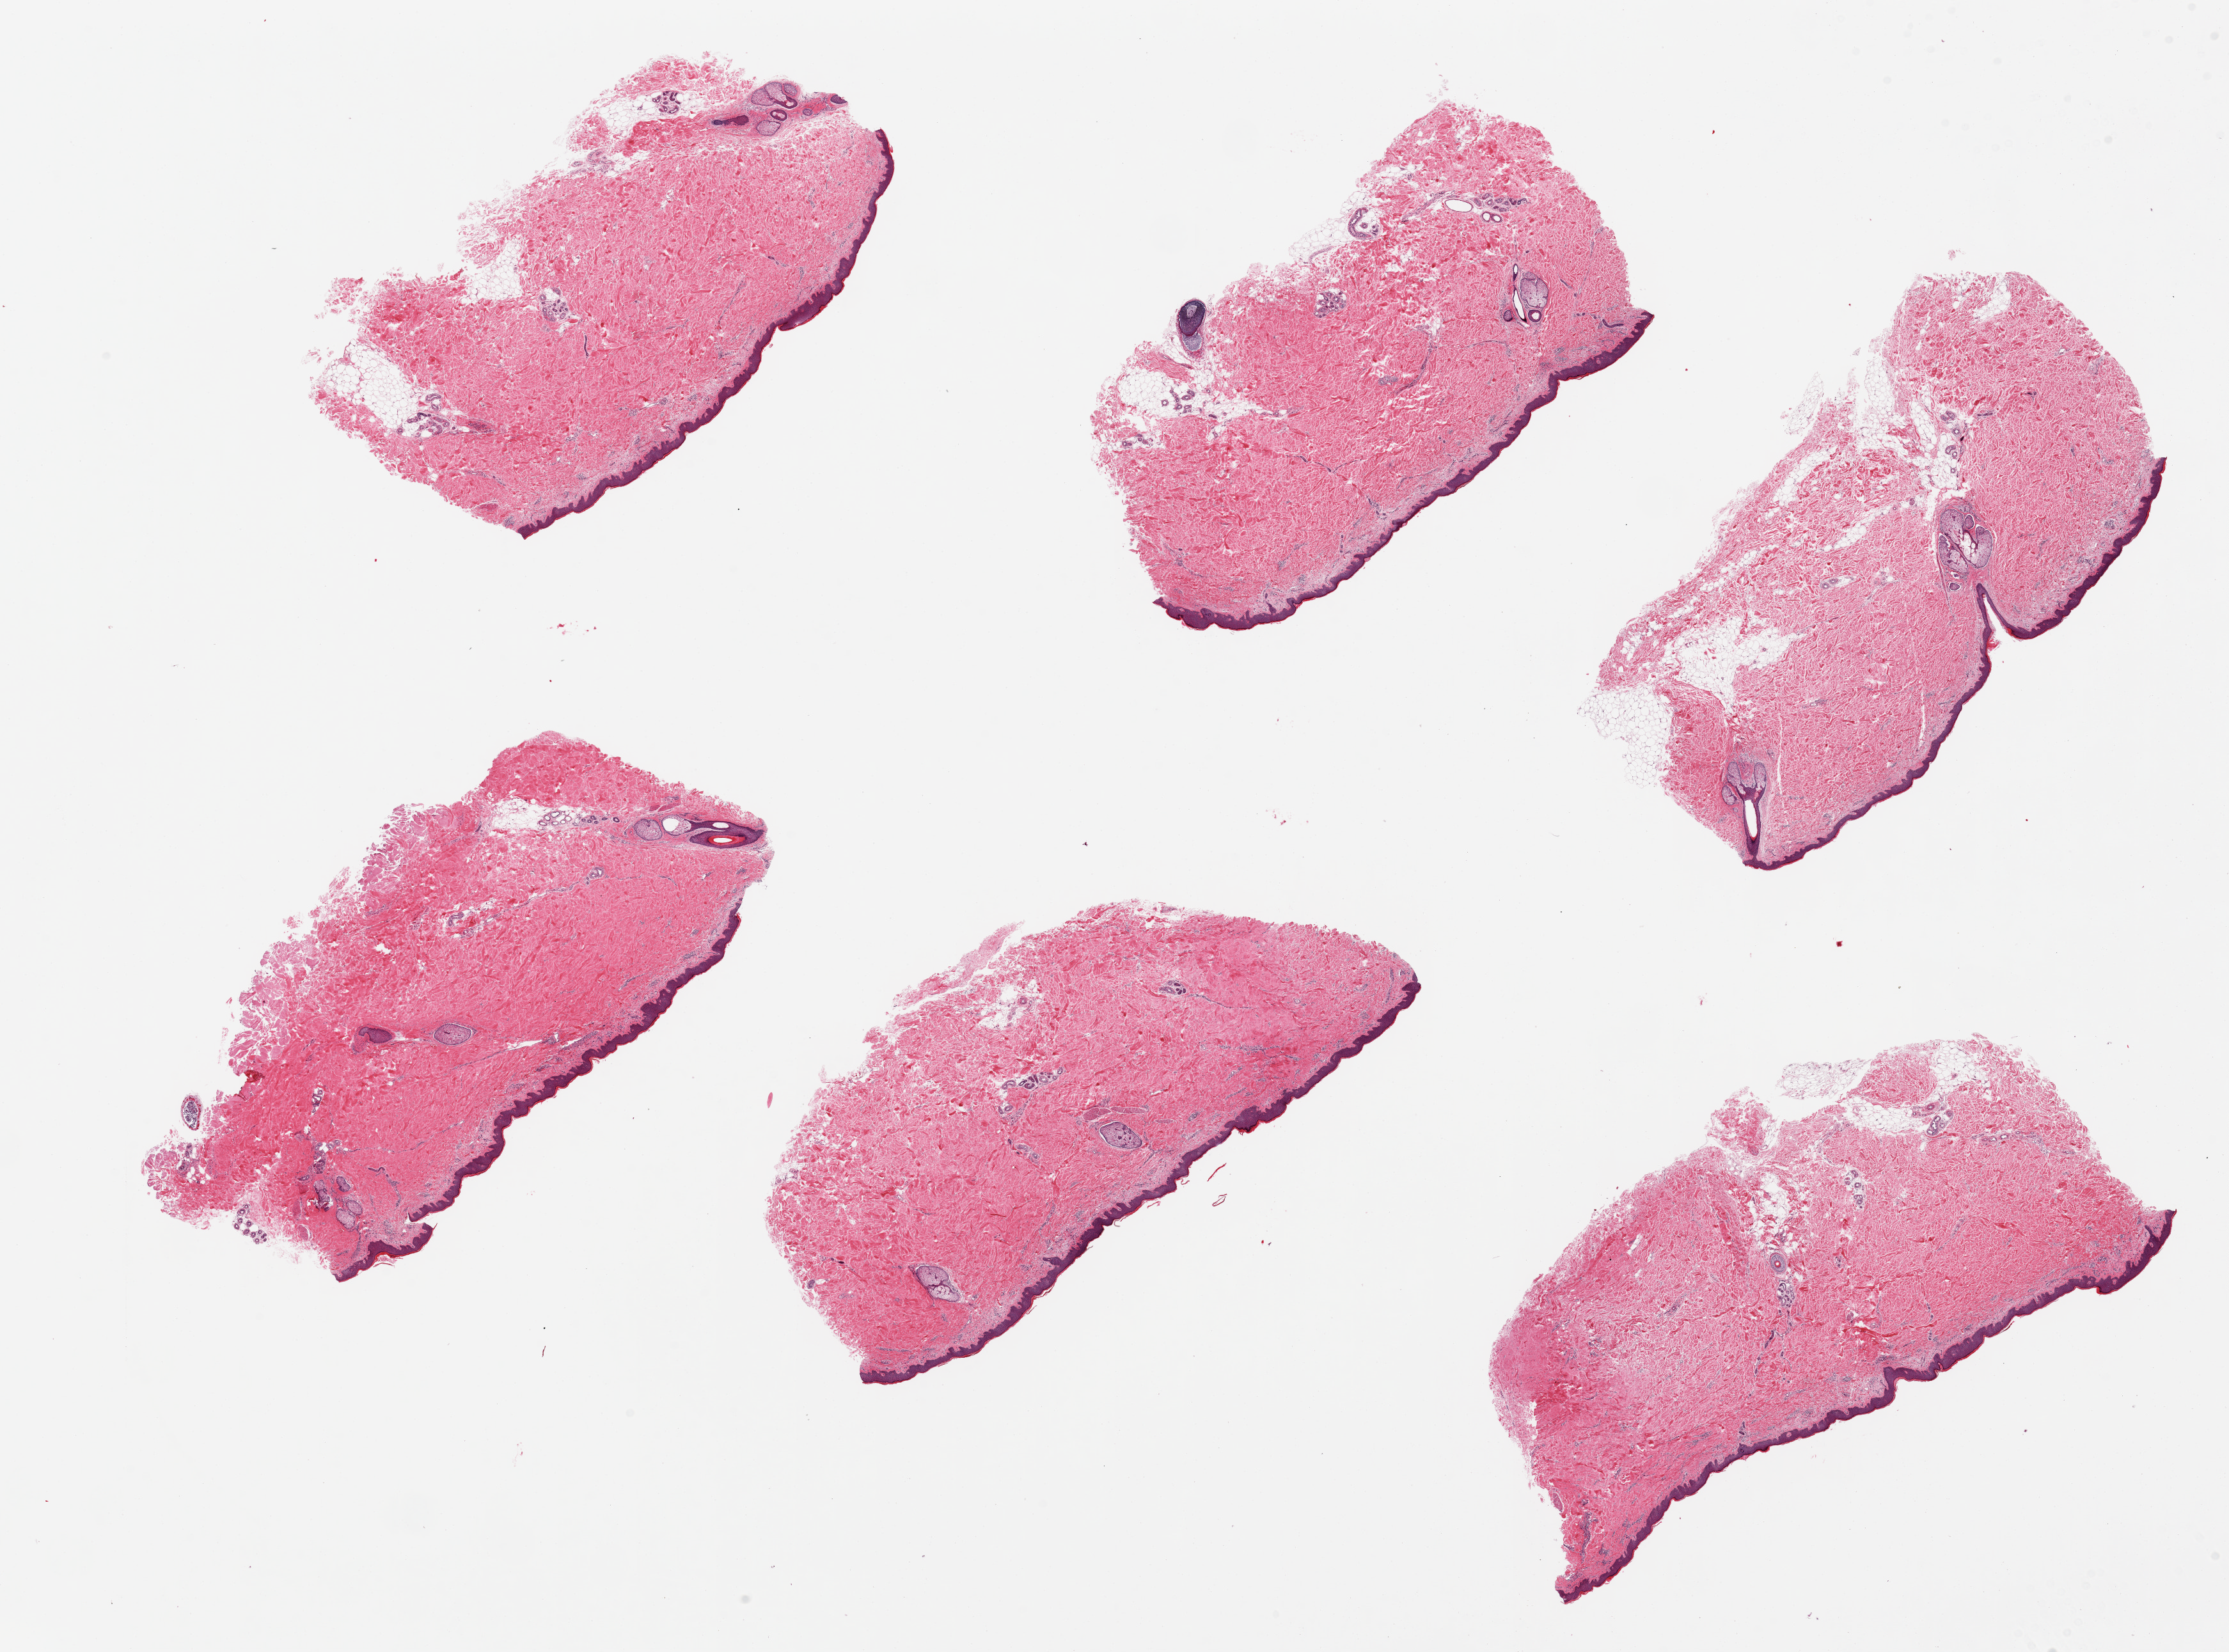
Digitized hematoxylin and eosin (H&E)-stained section, brightfield — whole scanned area (about 27.6 x 20.4 mm, from a 20x scan) shown as a low-resolution overview. PAXgene-fixed, paraffin-embedded tissue. Sampled site (target tissue): skin of suprapubic region. Donor tissue sample. Donor sex: male.
Review note (as recorded): 6 pieces; relatively well-trimmed, 3 with adipose tissue (internal and attached) of 5-10%.